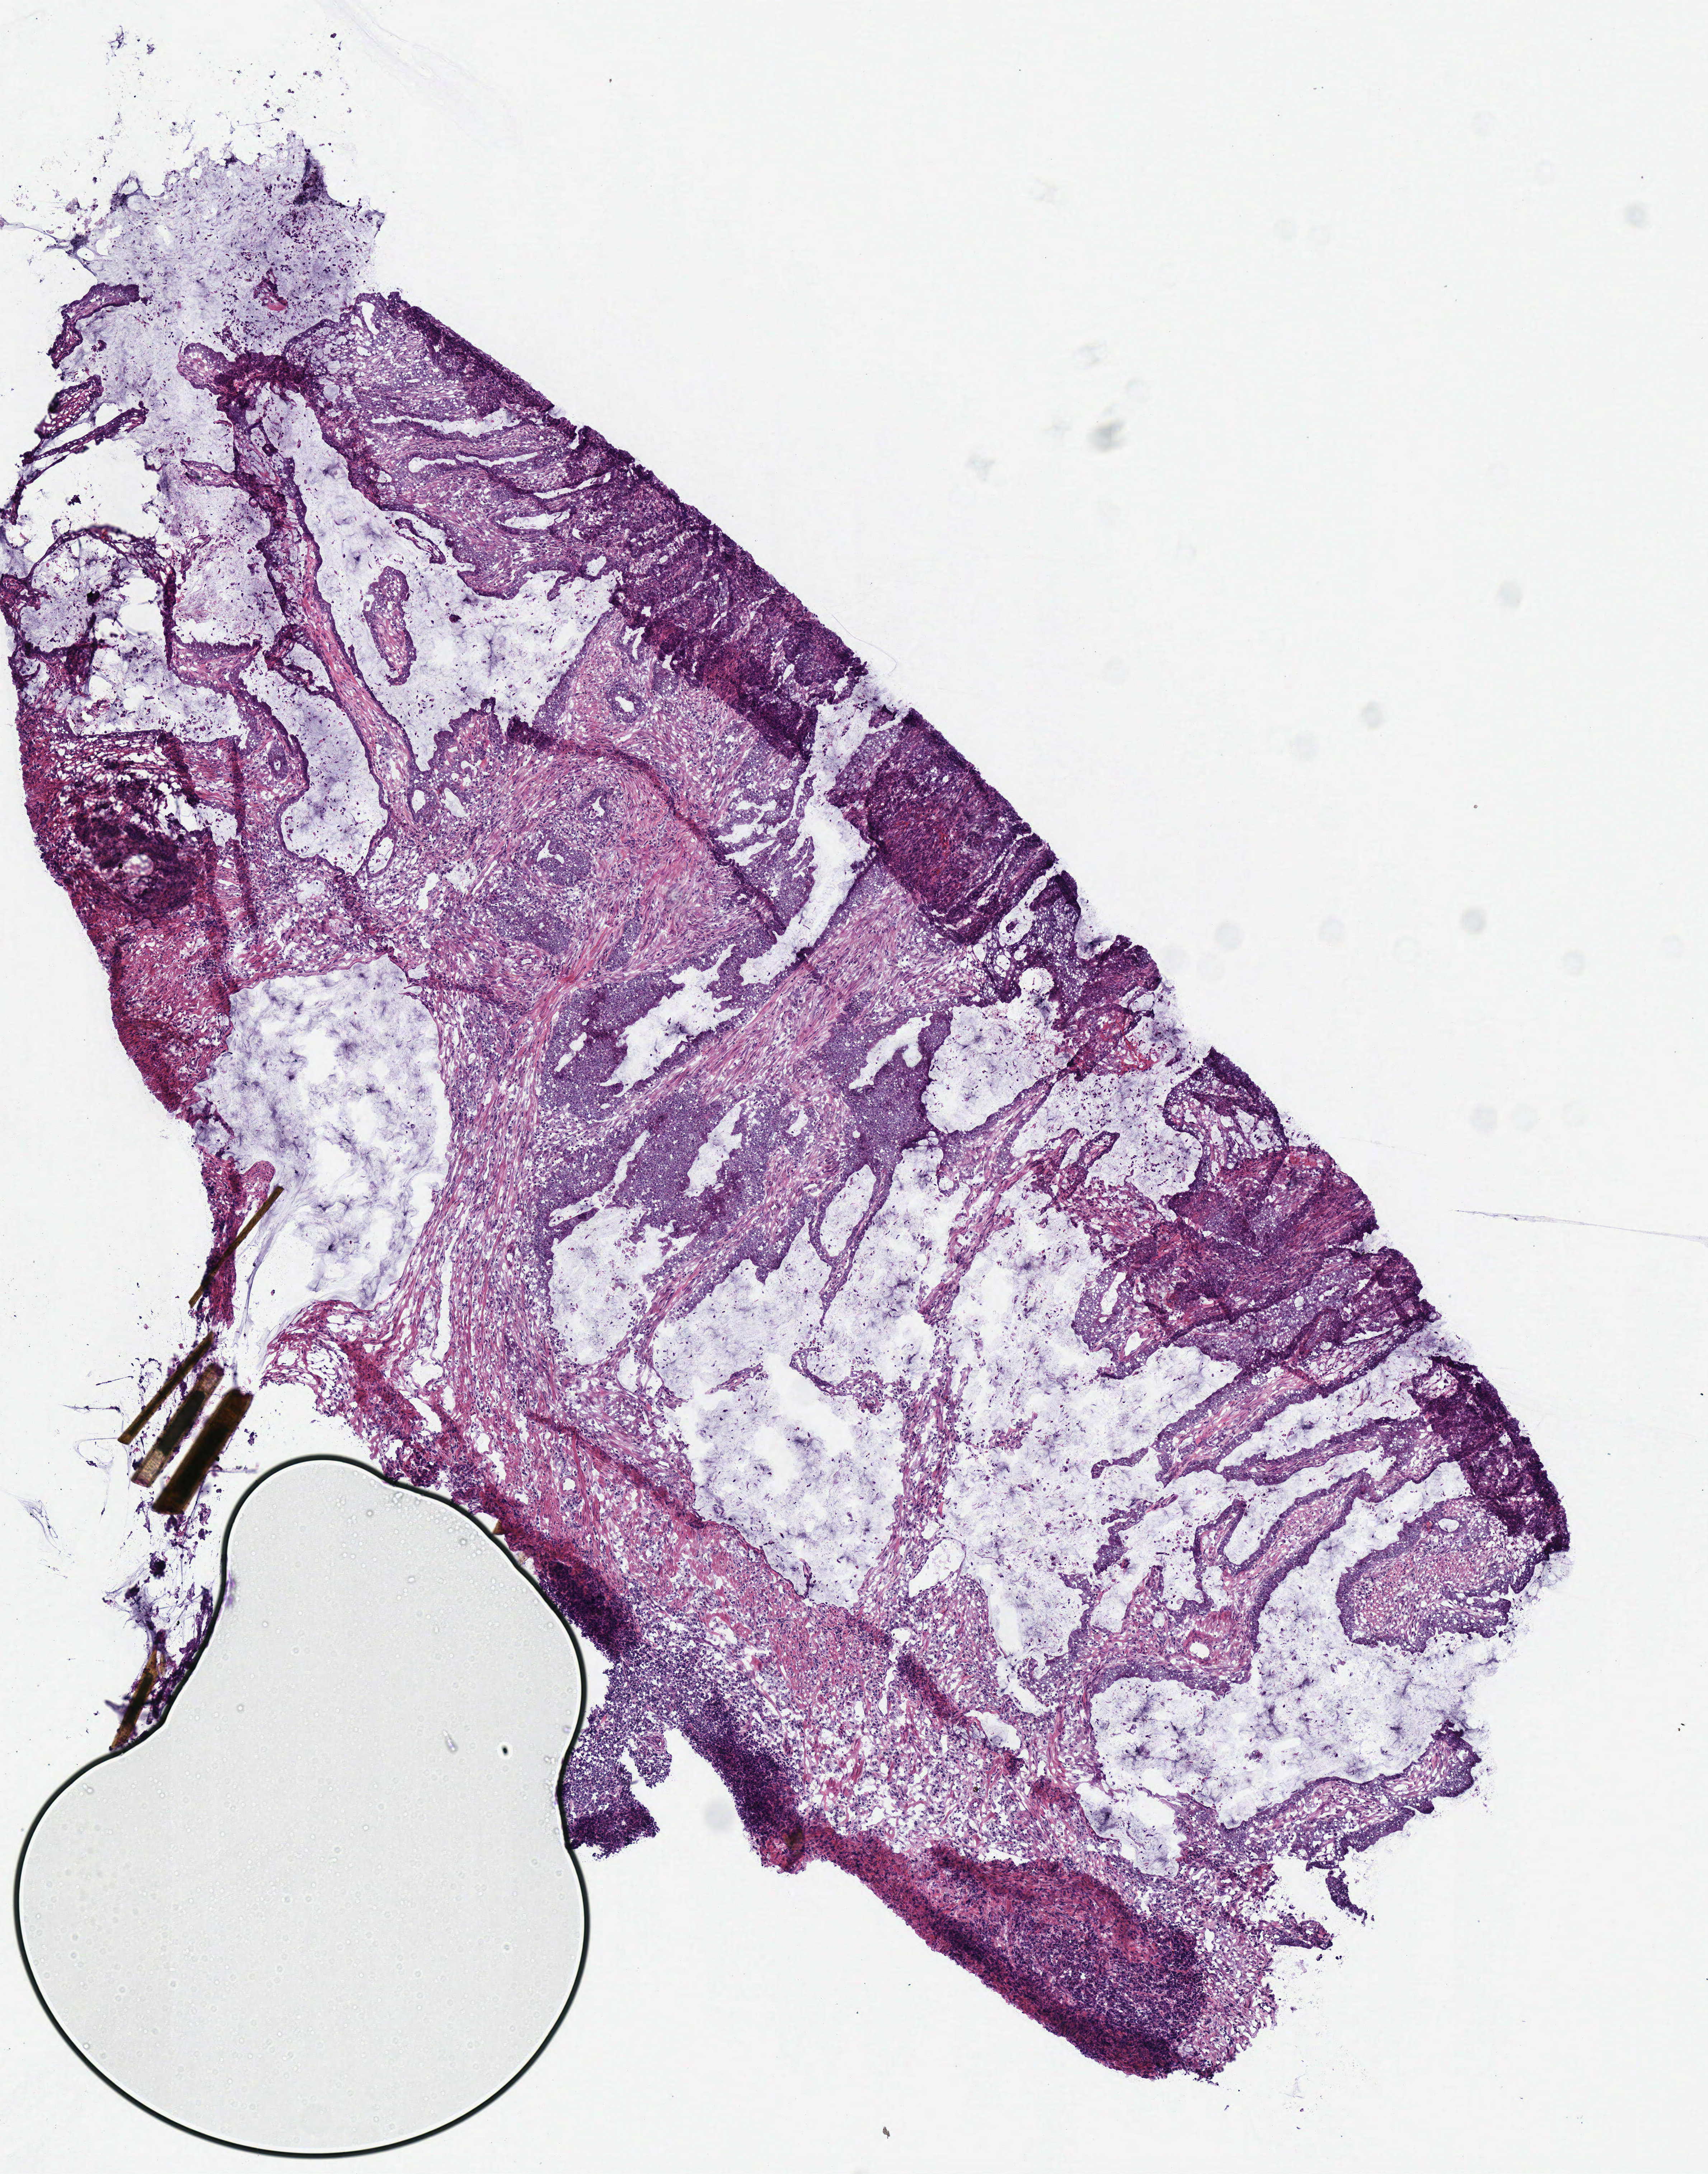
Digitized H&E tissue section (whole slide) — shown as a low-resolution overview of the whole scanned area (about 4.7 x 6.0 mm, slide scanned at 40x). Frozen section from the bottom of the tissue portion. Primary tumour sample from the colon. Patient: male, age at initial diagnosis 67 years. Slide review estimates, as recorded: tumour cells 75%, tumour nuclei 75%, normal cells 0%, stromal cells 23%, necrosis 2%. Inflammatory infiltration, as recorded: lymphocyte infiltration 10%, monocyte infiltration 0%, neutrophil infiltration 2%.
TNM: T3 N0 M0. Lymph nodes positive (case pathology): 0 of 20 examined. Histologic diagnosis: Mucinous adenocarcinoma (cecum). AJCC pathologic stage: IIA (7th edition).